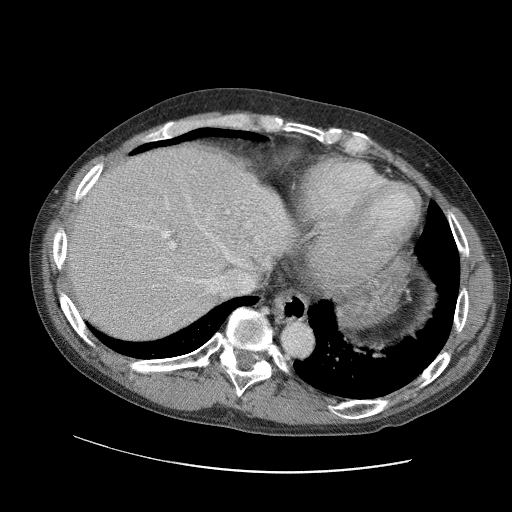
Contrast-enhanced abdominal CT (liver protocol), one axial slice. Position 82 of 109 along the scan axis. Reconstruction kernel STANDARD. Soft-tissue window (W 400 / L 40 HU). 2.5 mm slice thickness. 512 × 512 image matrix. From the clinical record (not read from this slice): diagnosis: hepatocellular carcinoma (patient treated with transarterial chemoembolisation; whether this scan precedes or follows treatment is not stated here); TNM stage (as recorded): Stage-IIIC; Child-Pugh class: B; tumour differentiation: well differentiated.
Annotated regions visible in this slice (semi-automatically segmented with operator editing):
- abdominal aorta: bounding box (x1, y1, x2, y2) in pixels: (283, 323, 313, 355)
- liver parenchyma outside the tumour (the mass and vessels are separate outlines, so this box may not span the whole liver): (62, 143, 306, 340)
- liver vessels: (102, 171, 293, 325)